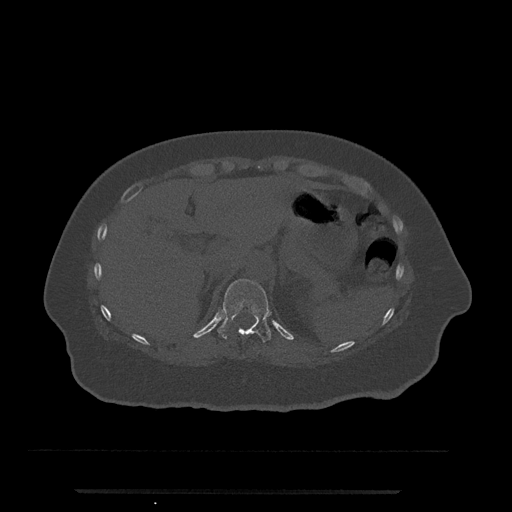
CT including the spine, one axial slice; position 233 of 797 along the scan axis; reconstruction kernel Br40s/3; 120 kVp; bone window (W 1800 / L 400 HU); 512 × 512 image matrix. Female patient, age 51 years. Case-level facts recorded for this patient, not image findings: primary cancer: neuro; vertebrae with lytic lesions (as recorded): T8.
Structures marked on this image (semi-automatic segmentation, software-assisted and operator-edited):
- T11 vertebra: bounding box [x1, y1, x2, y2] px = [218, 279, 271, 343]